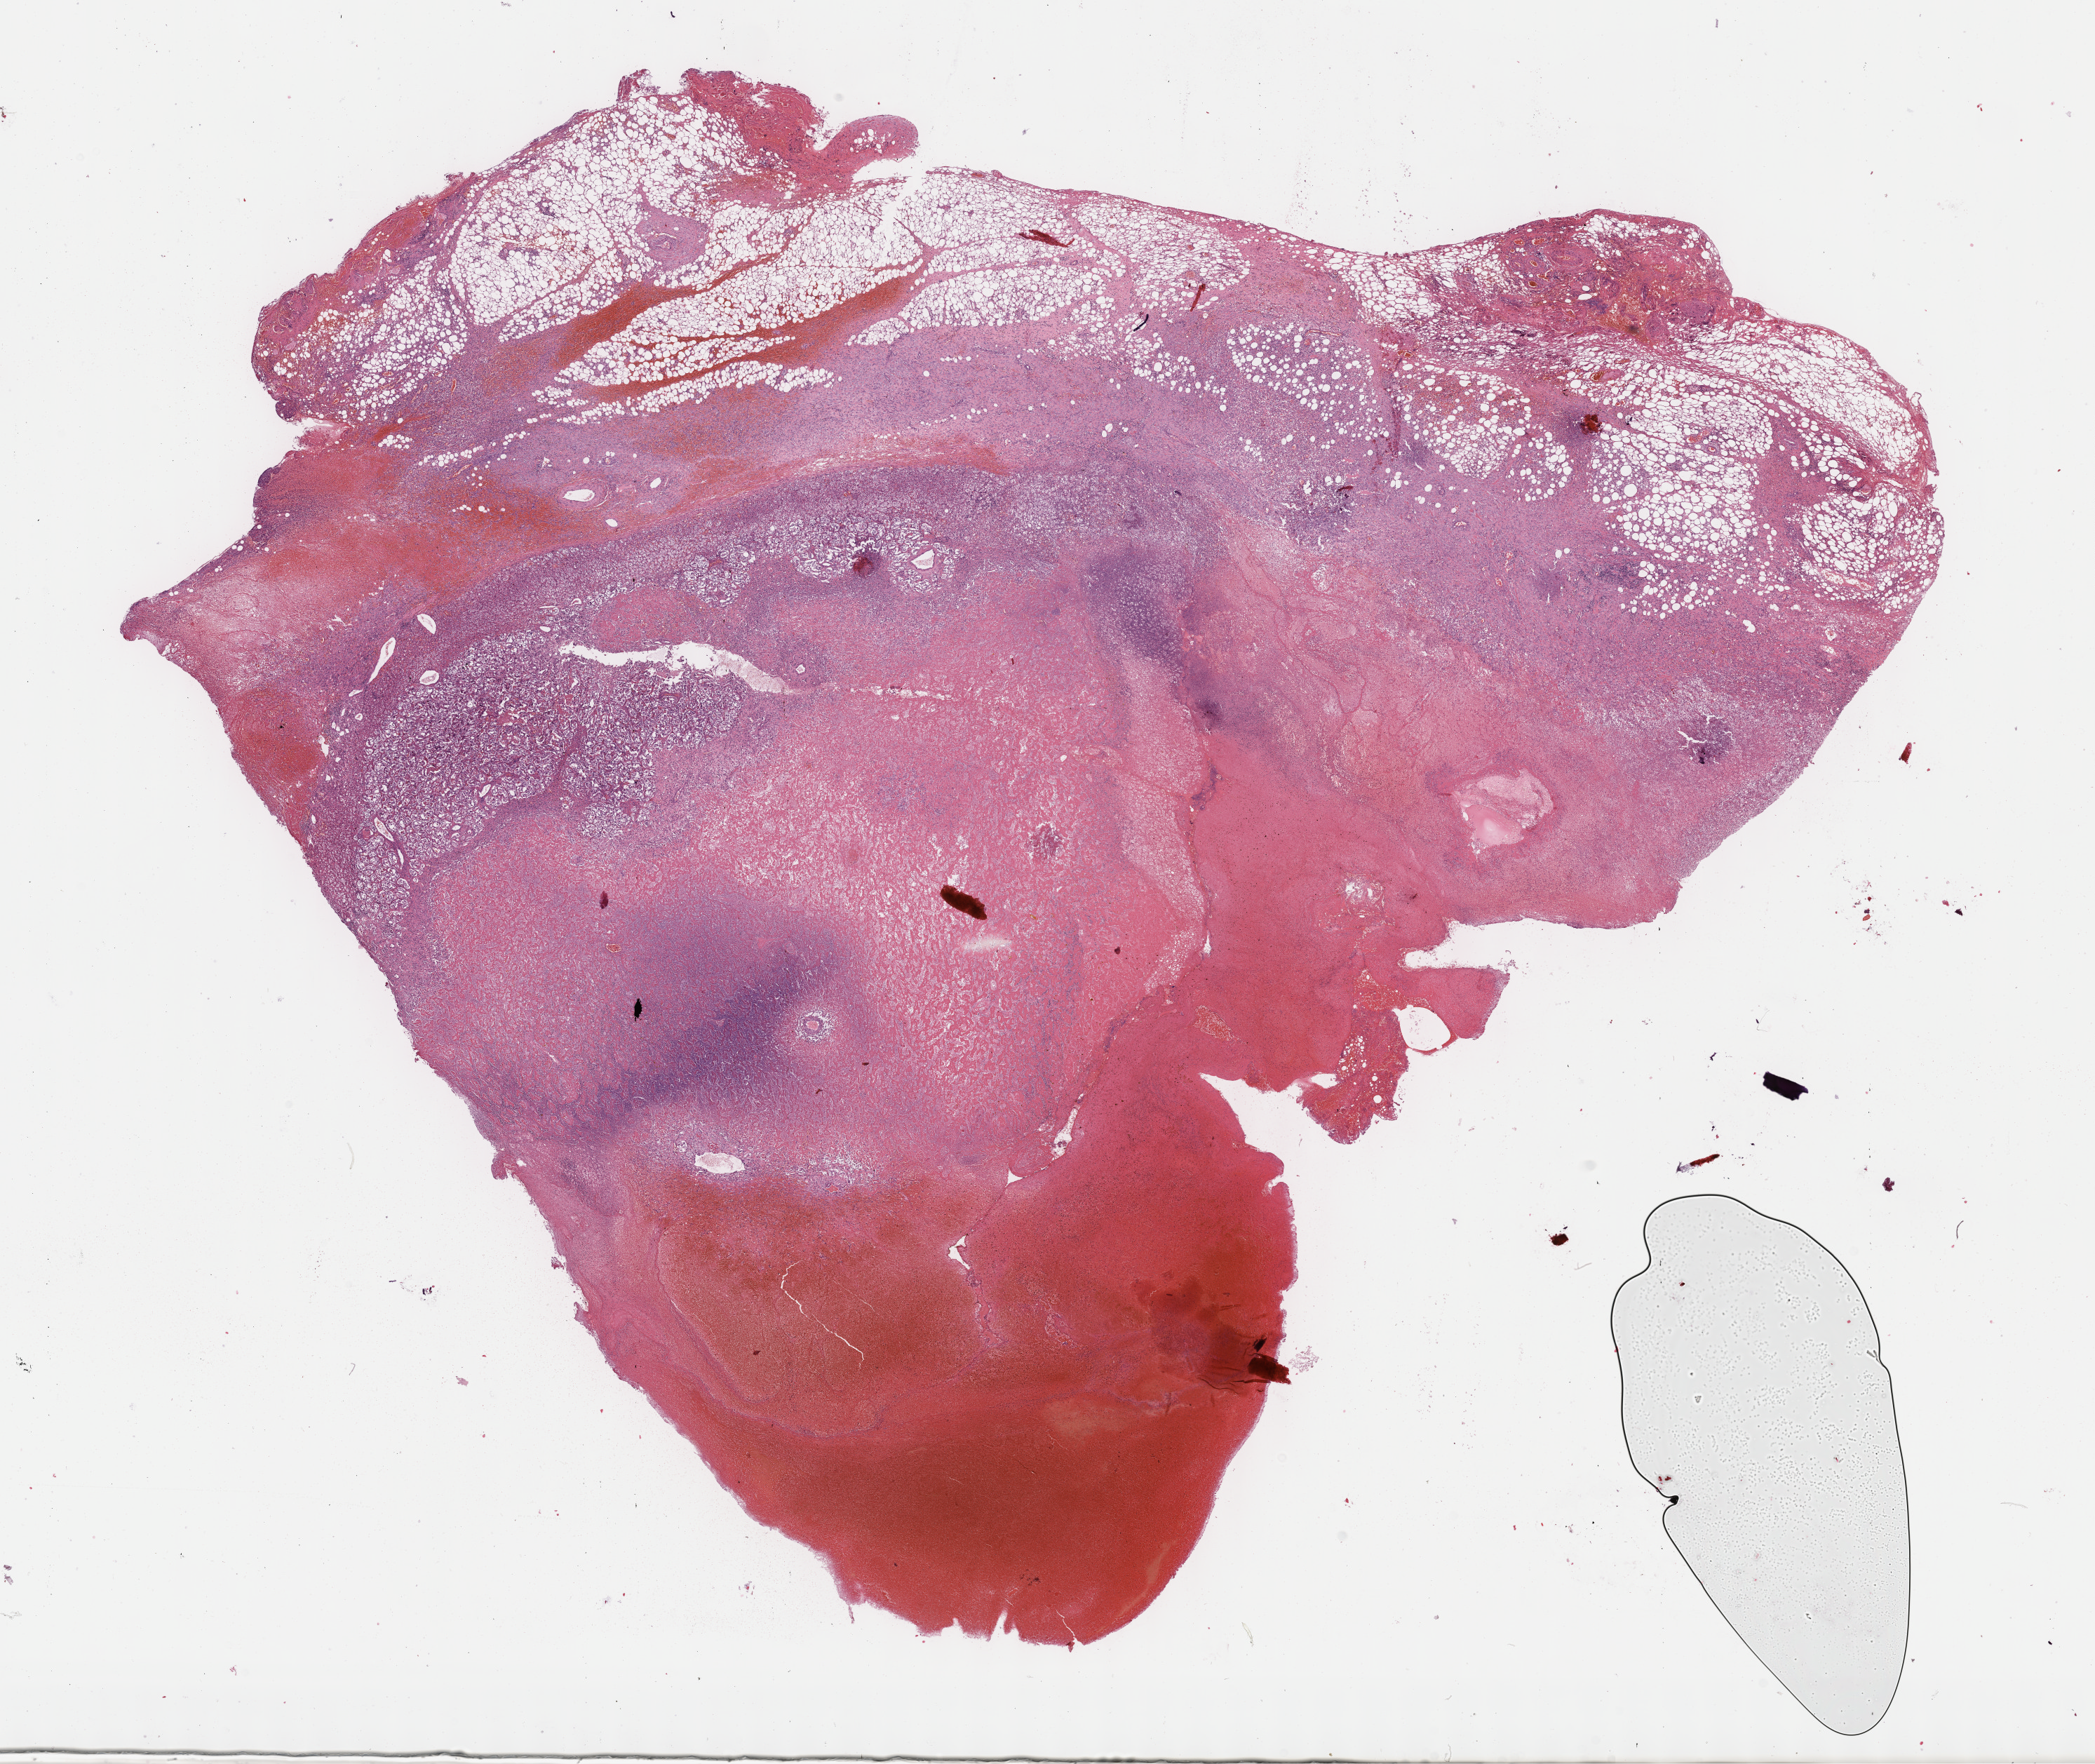
H&E-stained whole-slide image — whole scanned area (about 24.2 x 20.3 mm, from a 40x scan) shown as a low-resolution overview, FFPE section, sample: primary tumour, adrenal gland. Female, age 35 years at initial diagnosis.
Diagnosis: Pheochromocytoma, malignant.